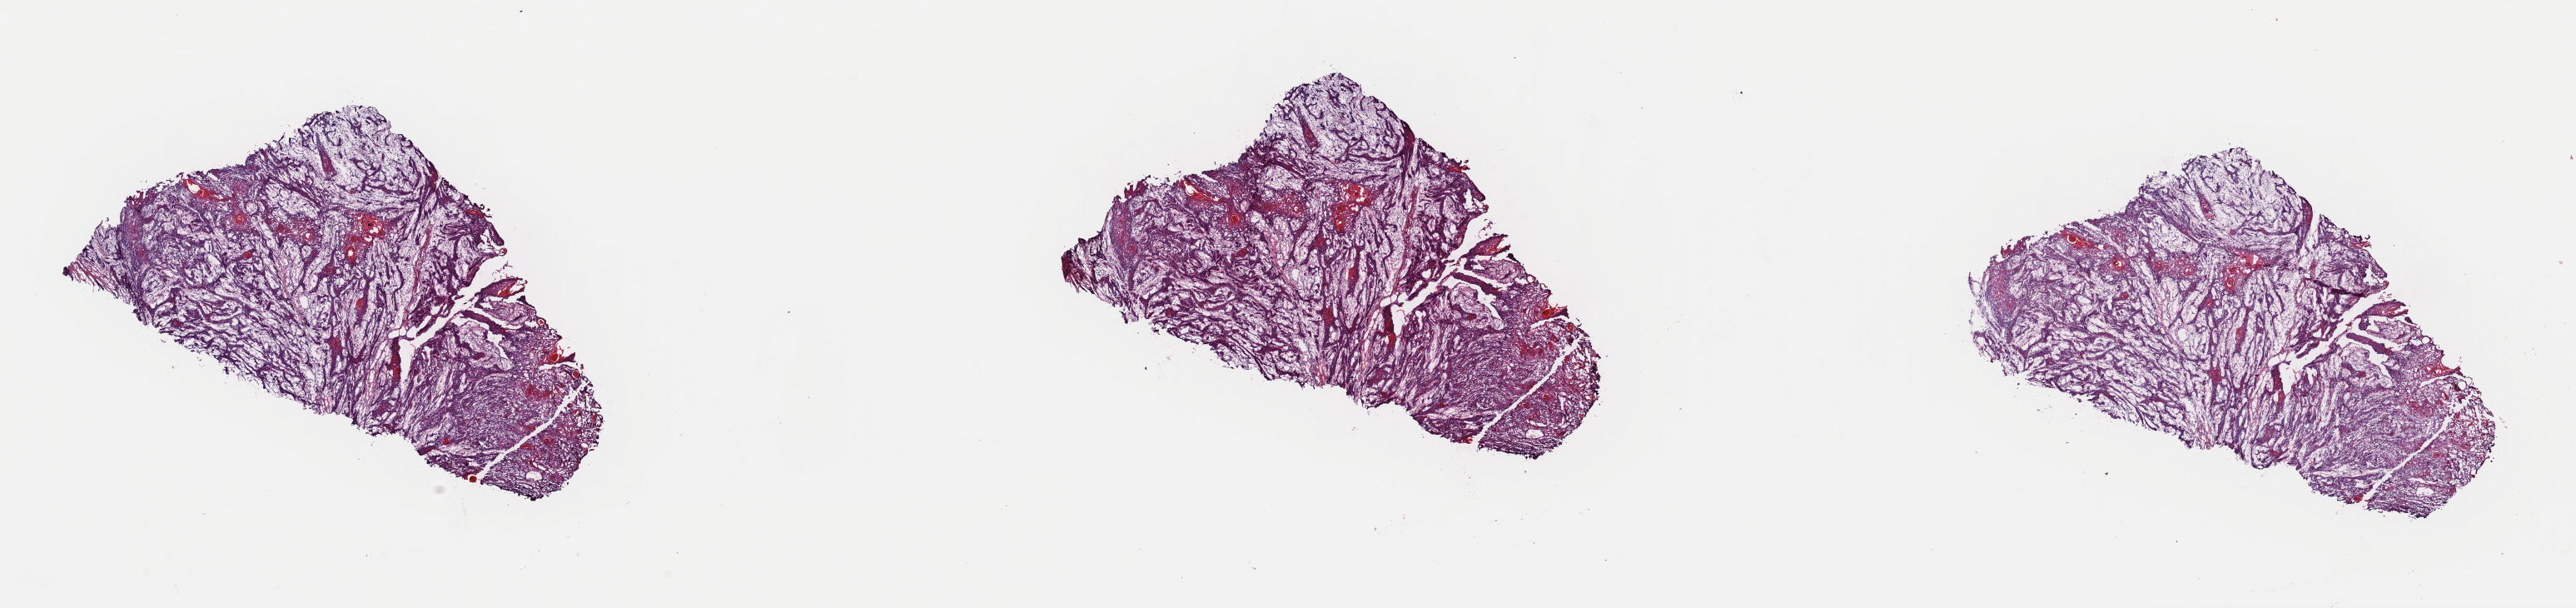
H&E-stained whole-slide image, shown as a low-resolution overview of the whole scanned area (about 24.4 x 5.8 mm, acquisition: 40x scan), frozen section, head and neck, primary tumour sample. Patient: male, age at initial diagnosis 45 years. Histologic grade: G2 (moderately differentiated). Composition of this section per pathologist review: tumour cells 40%, tumour nuclei 60%, normal cells 0%, stromal cells 55%, necrosis 5%. Inflammatory infiltration, as recorded: lymphocyte infiltration 0%, monocyte infiltration 0%, neutrophil infiltration 0%.
Laterality: left. Histologic diagnosis: Squamous cell carcinoma, NOS (cheek mucosa). TNM: T3 N2b MX. Lymph nodes positive (case pathology): 2 of 42 examined. AJCC pathologic stage: IVA.